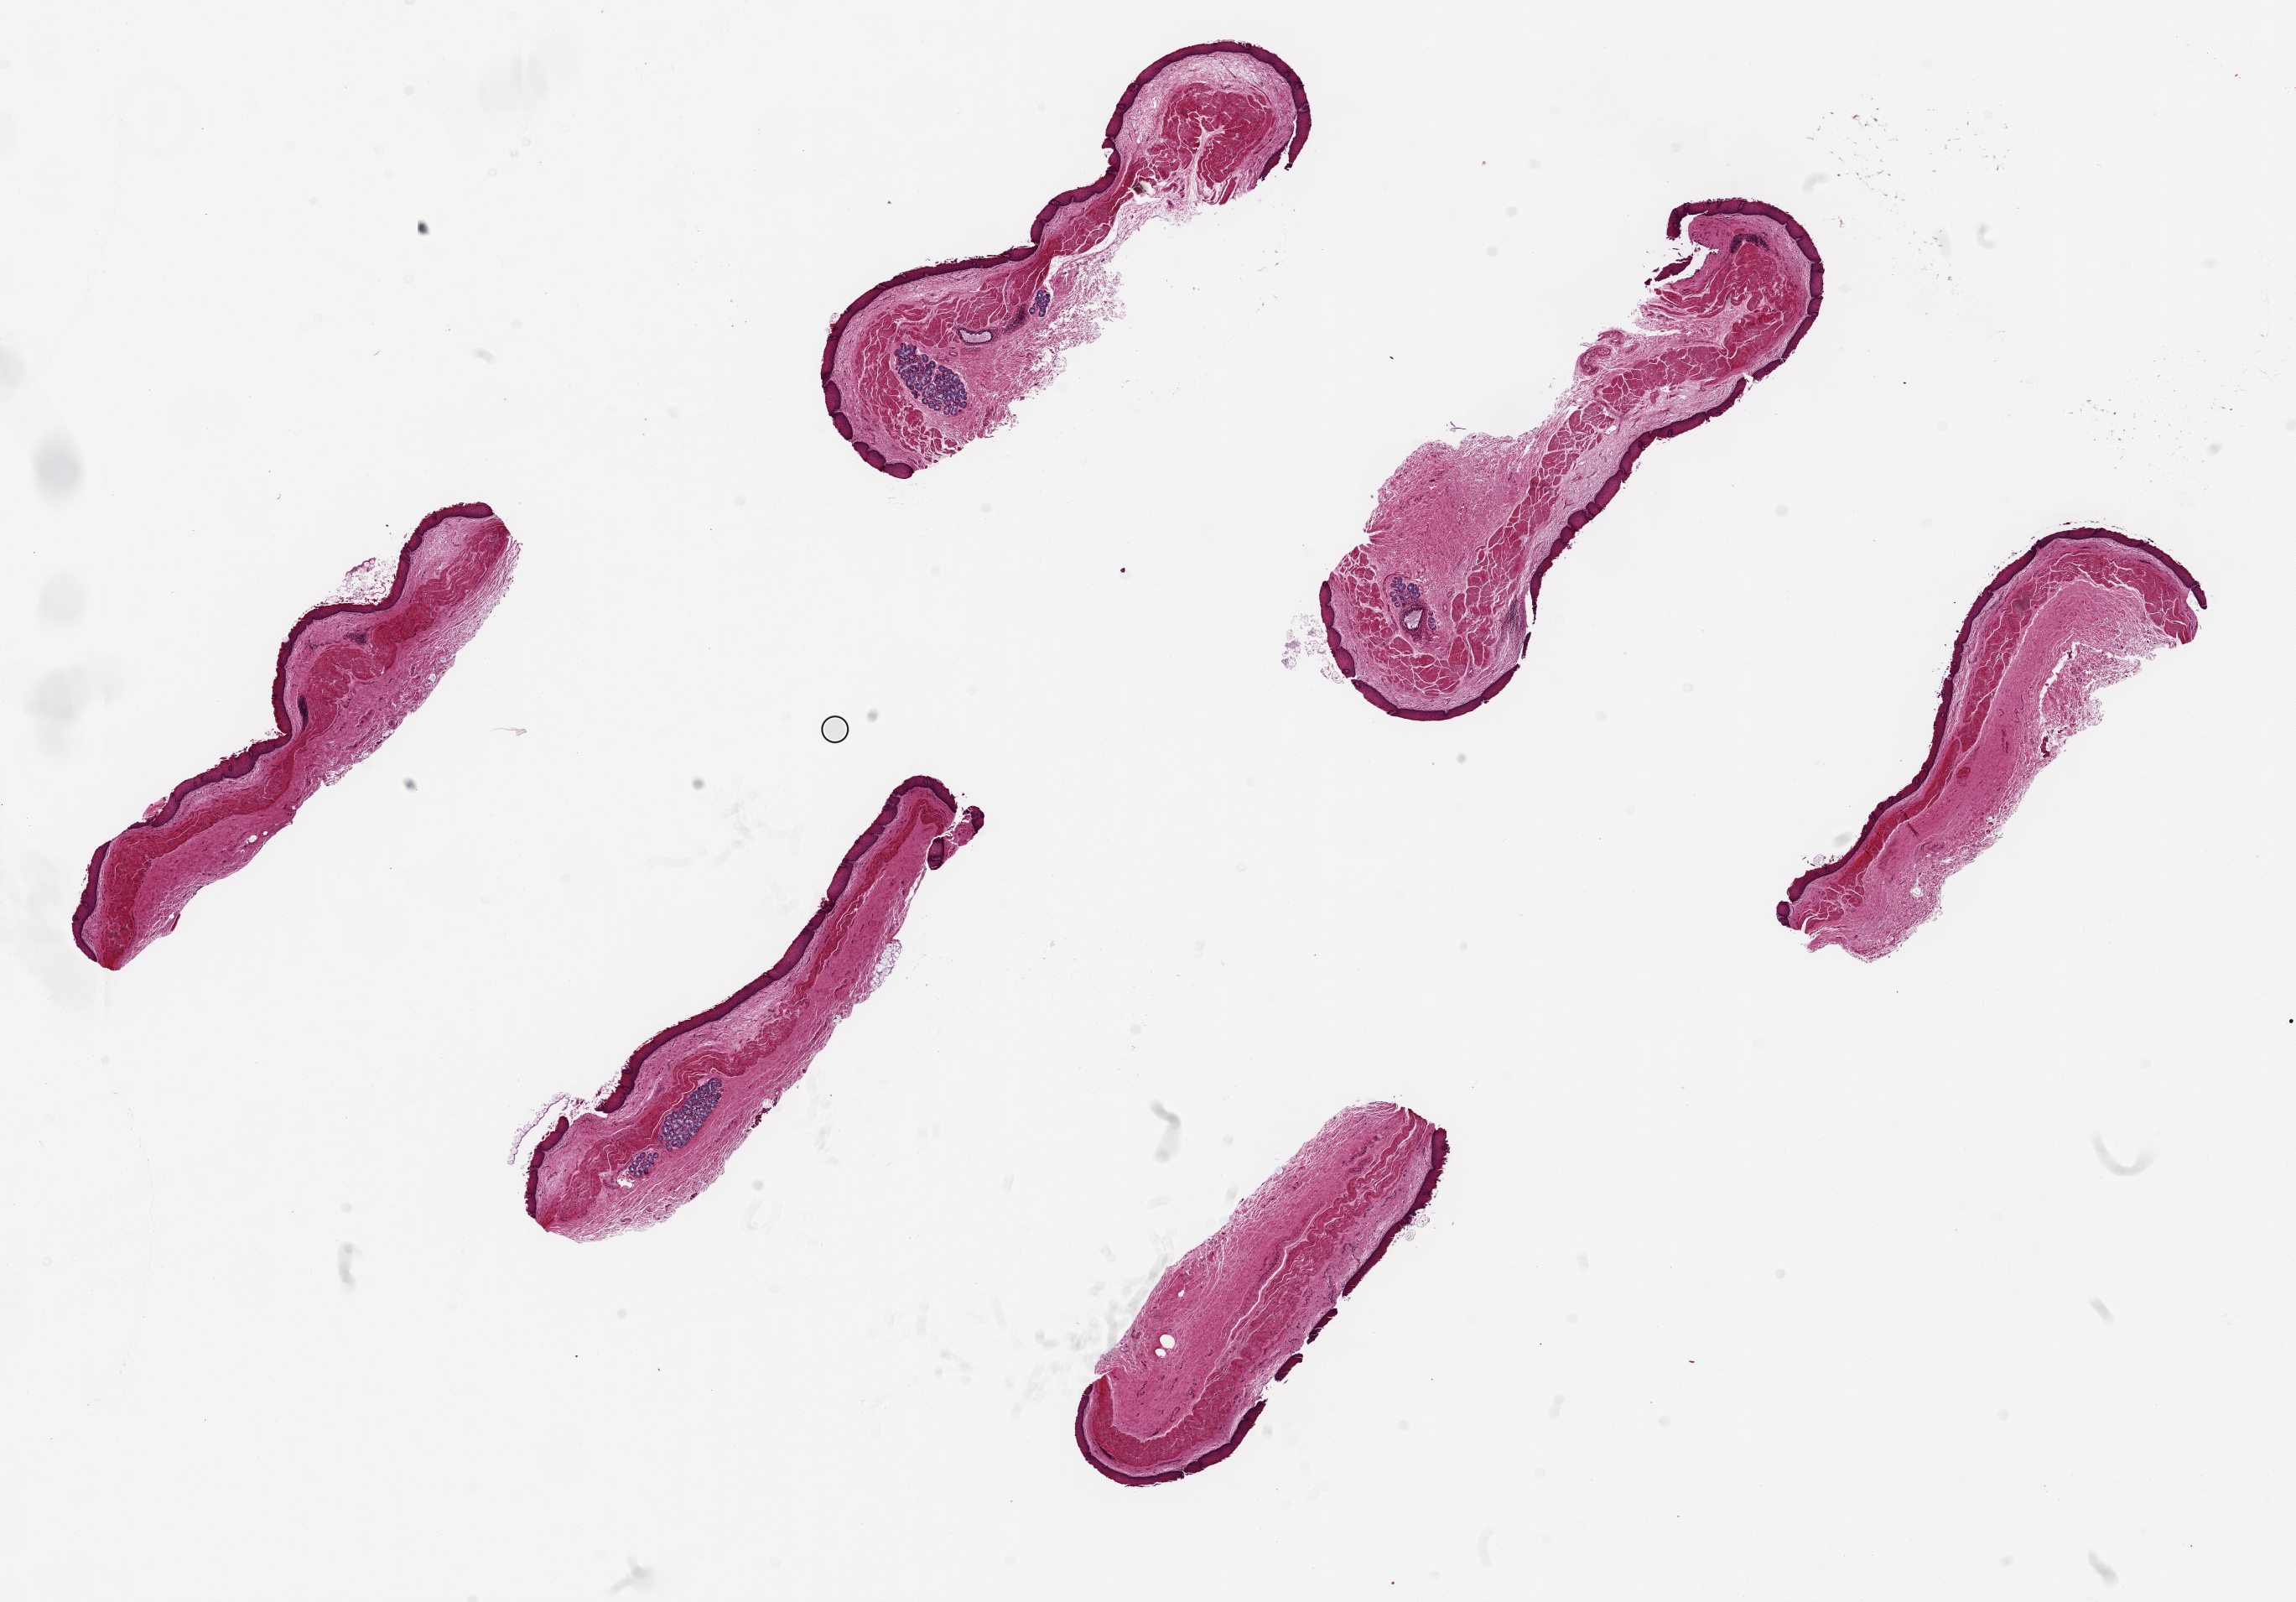
Whole-slide image, H&E stain, shown as a low-resolution overview of the whole scanned area (about 21.7 x 15.1 mm, slide scanned at 20x). PAXgene-fixed, paraffin-embedded tissue. Section of esophageal mucous membrane (target tissue). Donor tissue sample. Male donor.
• pathologist's review note for this sample: 6 pieces, ~5.5x1.5mm. Squamous mucosa is ~ 10-15% of thickness